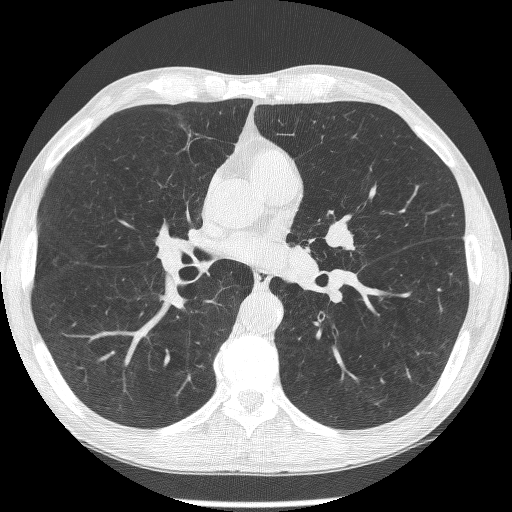
Chest CT (low-dose screening protocol), one axial image, second annual screen, lung window (W 1500 / L -600 HU), 1.25 mm slice thickness, slice 142 of 293 in the series. Male, age 62 years at enrolment. Former smoker at enrolment.
• Expert-annotated lung lesion, bounding box [x1, y1, x2, y2] px = [318, 217, 367, 265].
• The screening reader recorded 2 non-calcified nodules or masses ≥4 mm on this exam; which of them this box marks is not recorded.
• Later outcome: lung cancer diagnosed 95 days after this screen — small cell carcinoma, NOS, left upper lobe, stage IIIA (AJCC 6th edition).